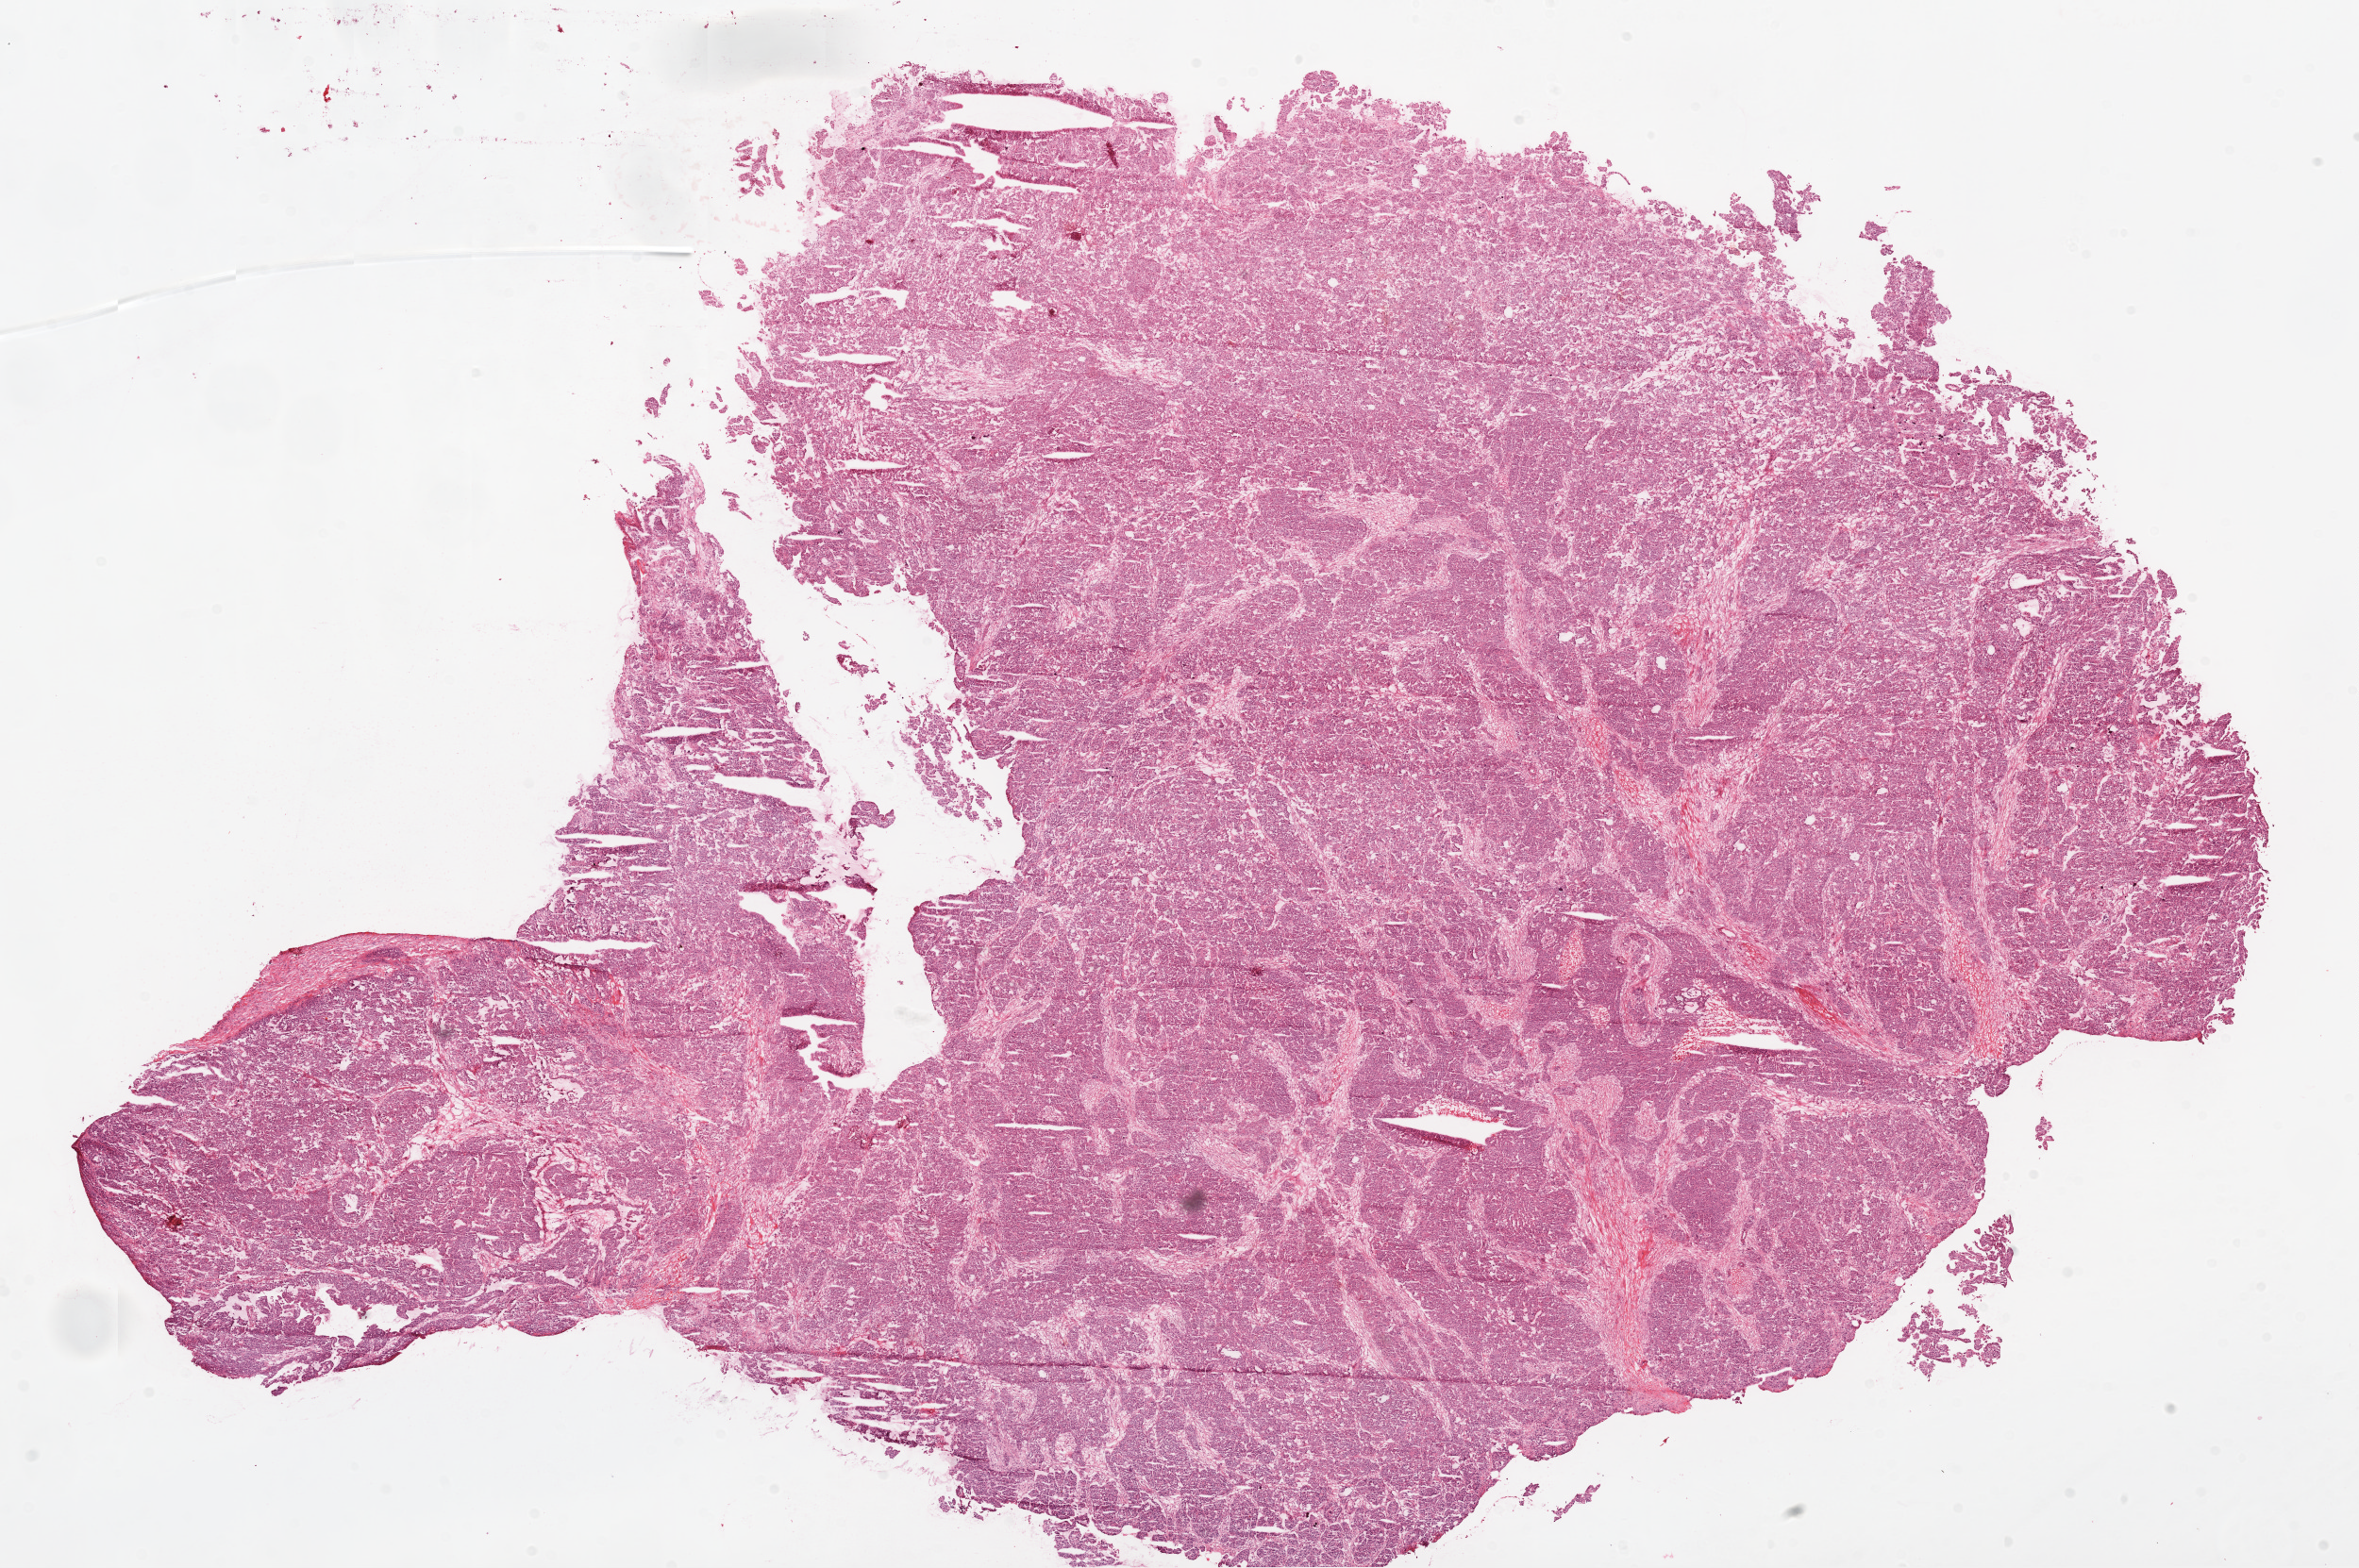
Whole-slide histology image, Hematoxylin and eosin (H&E) stained — a low-resolution overview of the entire scanned area, about 20.1 x 13.3 mm. Frozen section. Sample: recurrent tumour, ovary. Female patient; age at initial diagnosis 53 years. Slide review estimates, as recorded: tumour cells 95%, tumour nuclei 90%, normal cells 0%, stromal cells 5%, necrosis 0%. Inflammatory infiltration, as recorded: neutrophil infiltration 0%.
This section: recurrent tumour. Patient diagnosis: Serous surface papillary carcinoma.